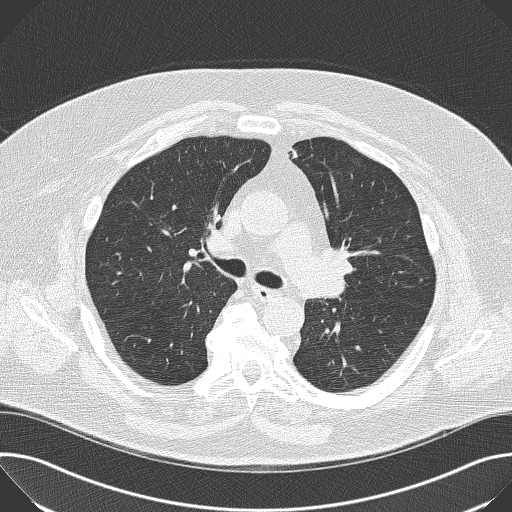
Chest CT (low-dose screening protocol), one axial image; first (baseline) screen; lung window (W 1500 / L -600 HU); 2 mm slice thickness; 512 × 512 image matrix. Male, age 68 years at enrolment.
Lesion marked by an expert reader, bounding box <318,232,372,283> (left, top, right, bottom; pixels). The screening reader recorded 2 non-calcified nodules or masses ≥4 mm on this exam; which of them this box marks is not recorded. Participant outcome: lung cancer diagnosed 638 days after this screen (after the second annual screen) — squamous cell carcinoma, NOS, left upper lobe, poorly differentiated (G3), stage IIB (AJCC 6th edition), 35 mm at pathology.